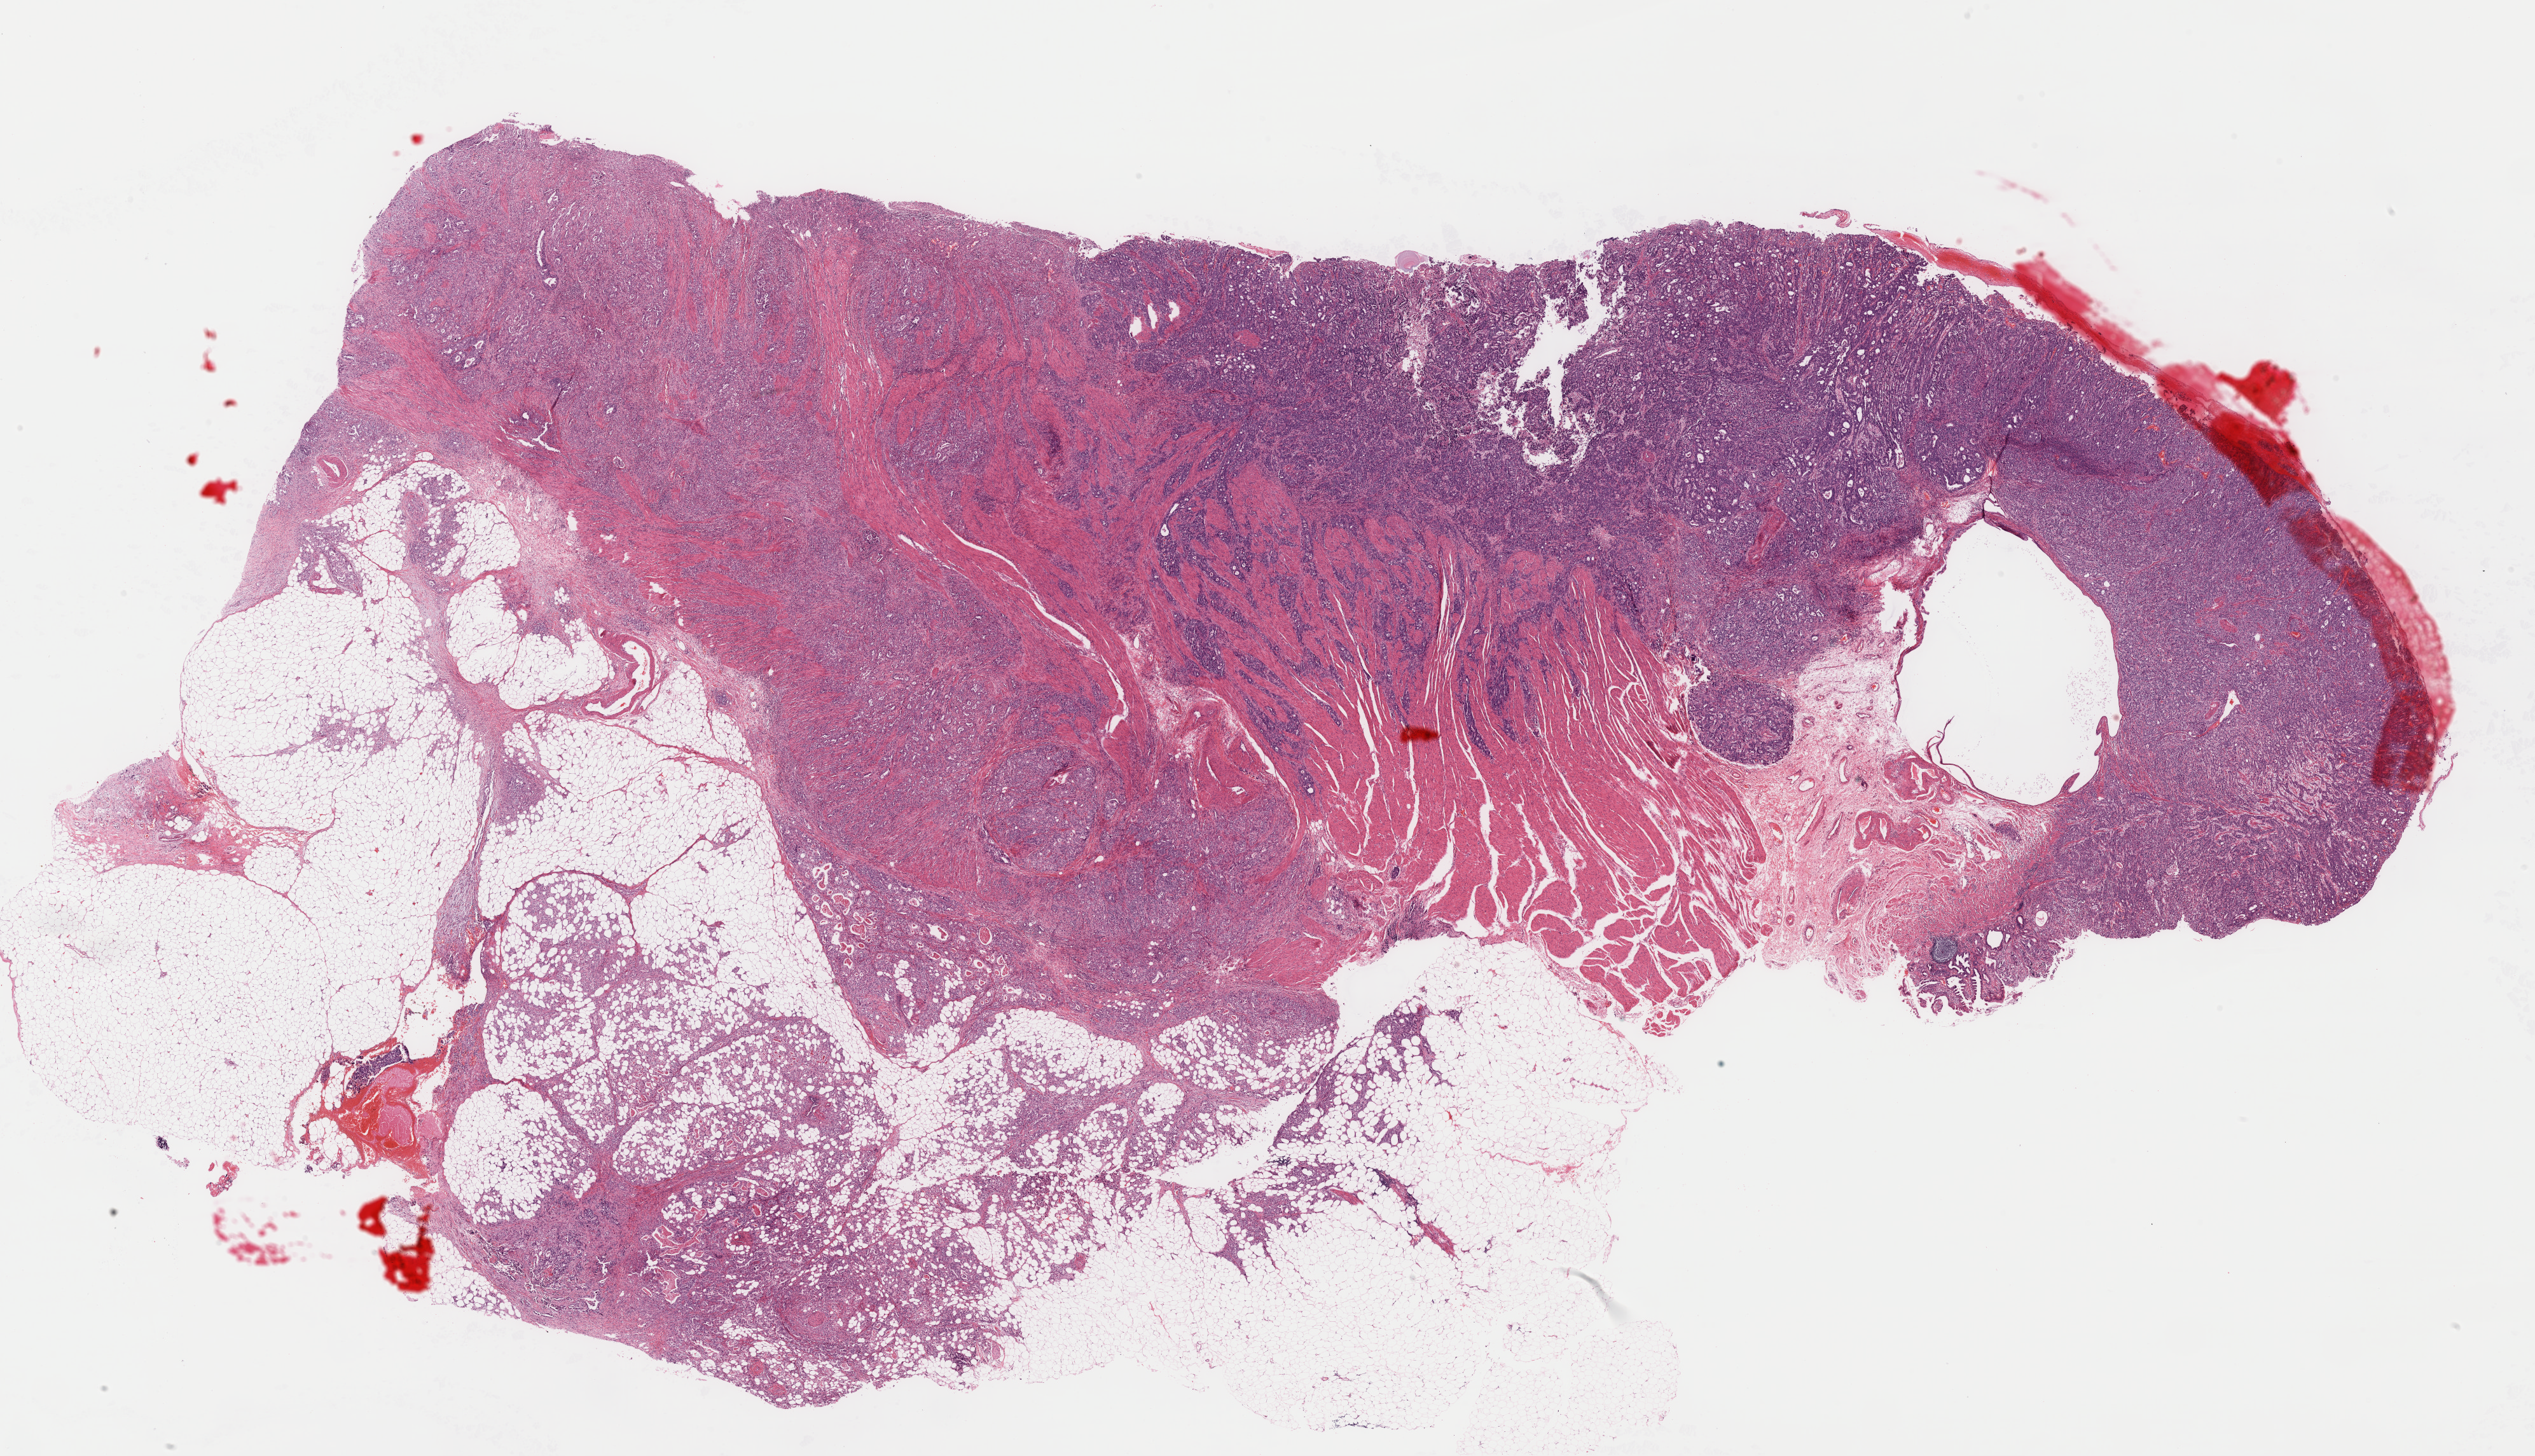
Whole-slide histology image, H&E-stained — a low-resolution overview of the entire scanned area, about 31.5 x 18.1 mm (acquisition: 40x scan); formalin-fixed paraffin-embedded (FFPE) diagnostic section; sample: primary tumour, stomach. Male, age 63 years at initial diagnosis. Histologic grade: G3 (poorly differentiated).
Lymph nodes positive (case pathology): 1 of 5 examined. Histologic diagnosis: Adenocarcinoma, NOS (gastric antrum). AJCC pathologic stage: IIIA (7th edition).